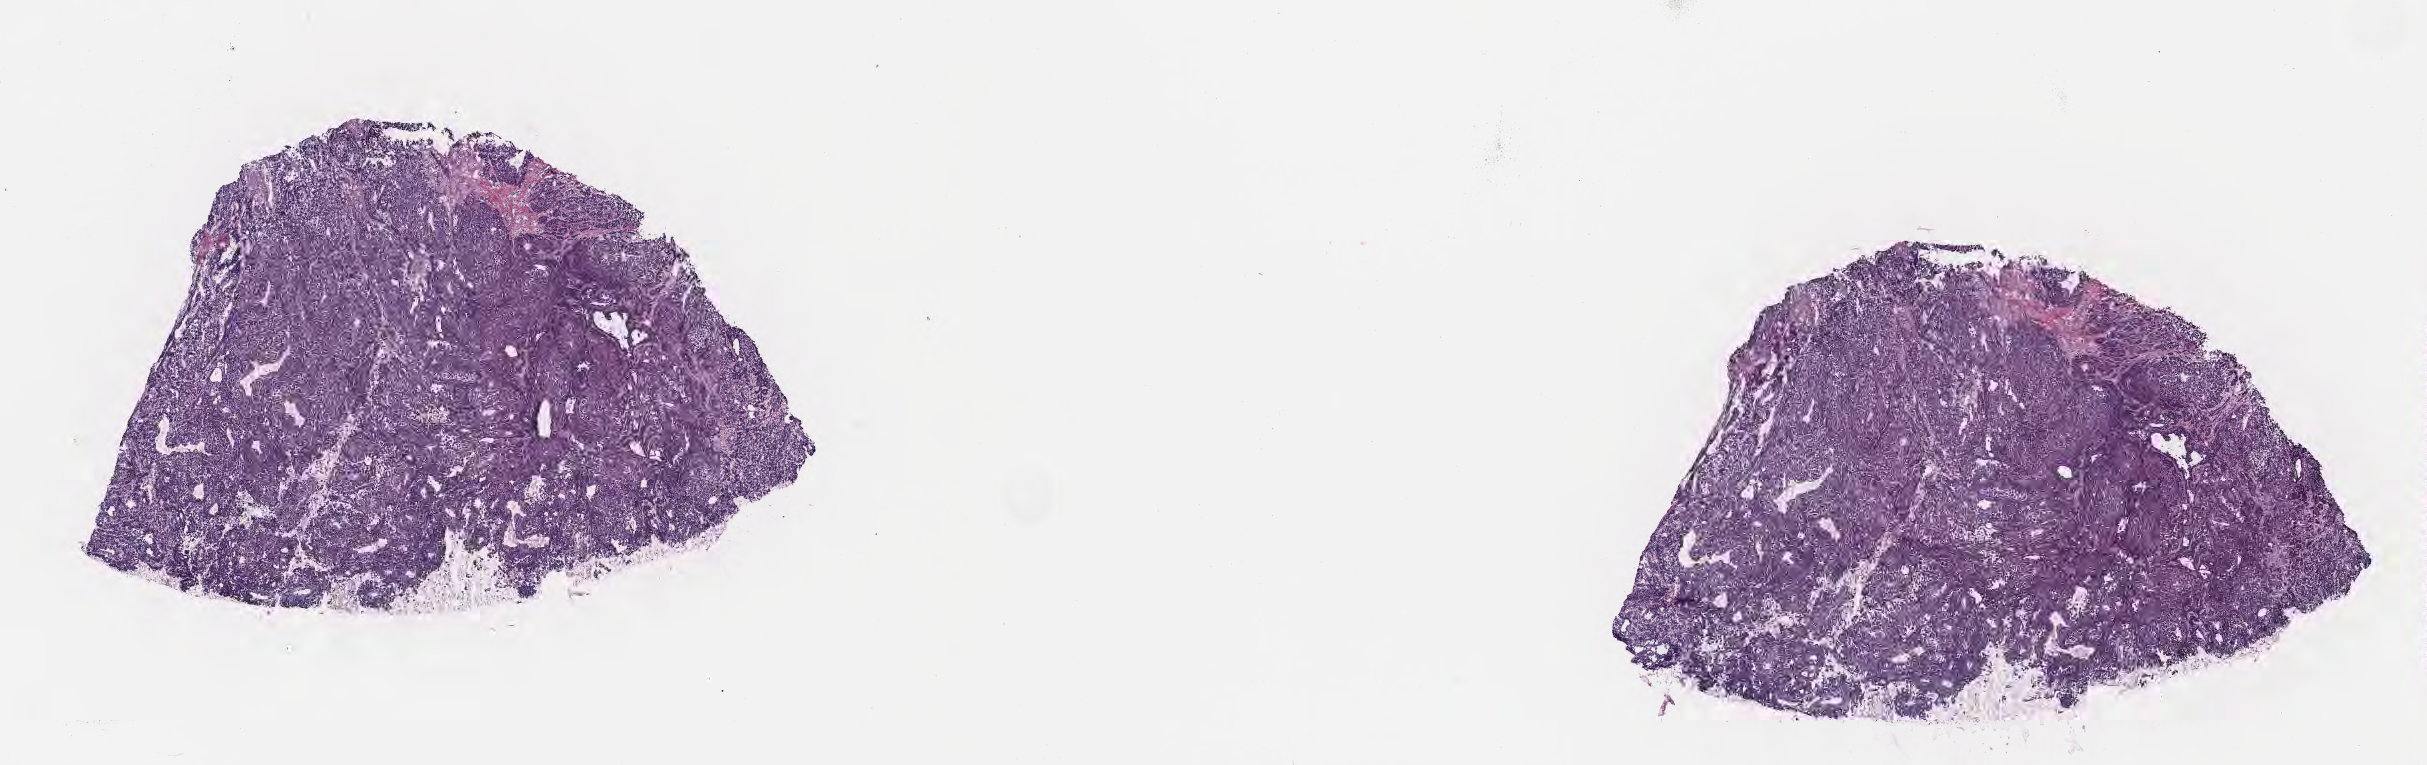
Digitized hematoxylin and eosin (H&E)-stained section, shown as a low-resolution overview of the whole scanned area (about 19.6 x 6.2 mm); frozen section; primary tumor; anatomic site: upper lobe of right lung. Patient male; age 51 years. Slide review estimates, as recorded: tumor cells 90%, tumor nuclei 90%, stromal cells 5%, necrosis 0%, normal cells 5%. Inflammatory infiltration, as recorded: lymphocyte infiltration 2%, monocyte infiltration 2%, neutrophil infiltration 0%.
Diagnosis: Solid carcinoma, NOS. AJCC pathologic stage: Stage IIA.